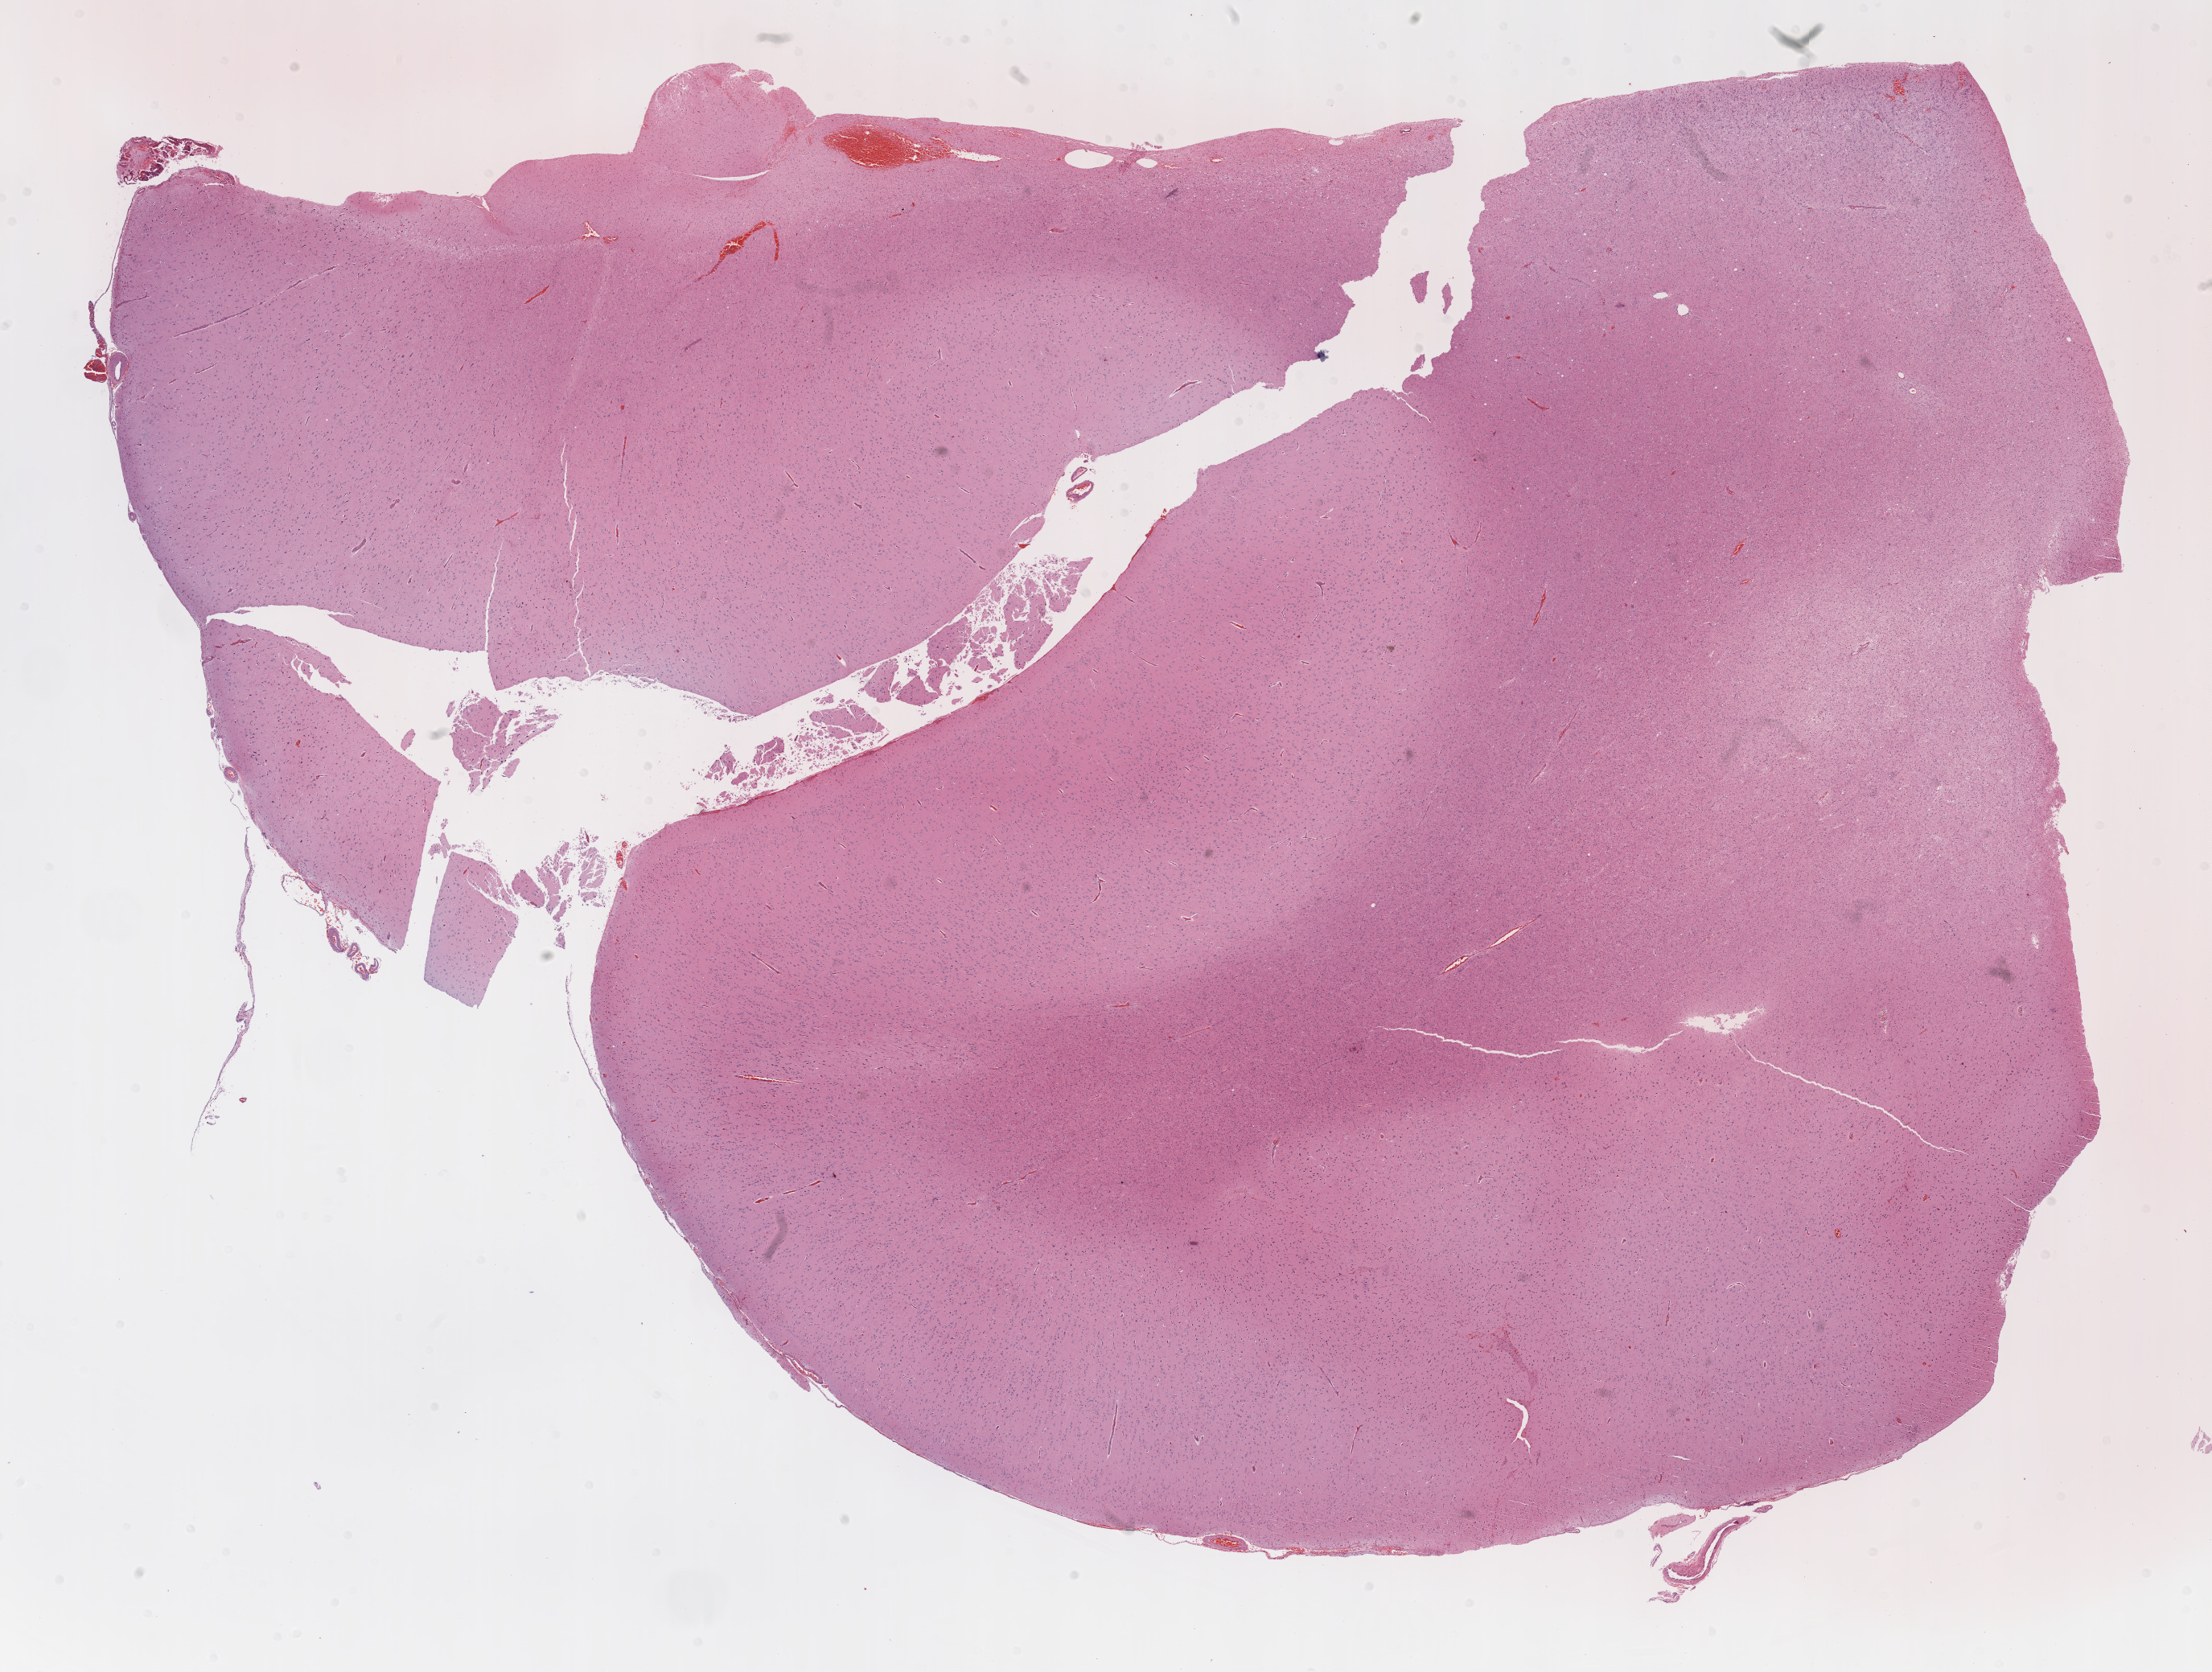
Whole-slide histology image, H&E — whole scanned area (about 22.1 x 16.7 mm, acquisition: 20x scan) shown as a low-resolution overview; formalin-fixed paraffin-embedded (FFPE) diagnostic section; brain, primary tumour sample. Male, age 71 years at initial diagnosis.
• pathologic diagnosis: Glioblastoma